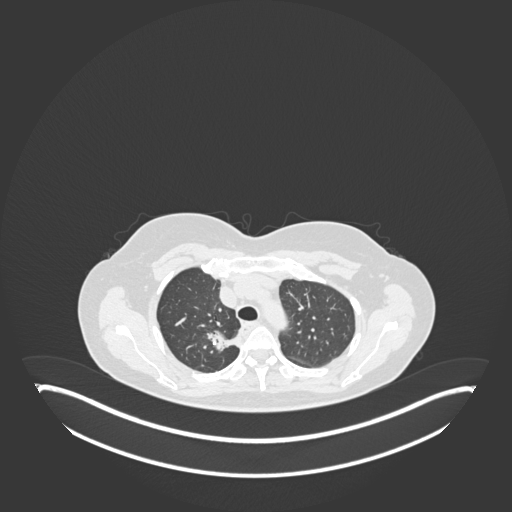
Chest CT, one axial slice. Slice 137 of 181 in the series (ordered by position). Reconstruction kernel B30f. 120 kVp. Lung window (W 1500 / L -600 HU). 512 × 512 image matrix, field of view 500 × 500 mm. Patient: female, 65 years. Case-level facts recorded for this patient, not image findings: clinical TNM (as recorded): T1b N0 M0.
Structures marked on this image (bounding box drawn by a radiologist):
- lung tumour (recorded histology: adenocarcinoma): bounding box (x1, y1, x2, y2) in pixels: (208, 329, 240, 356)